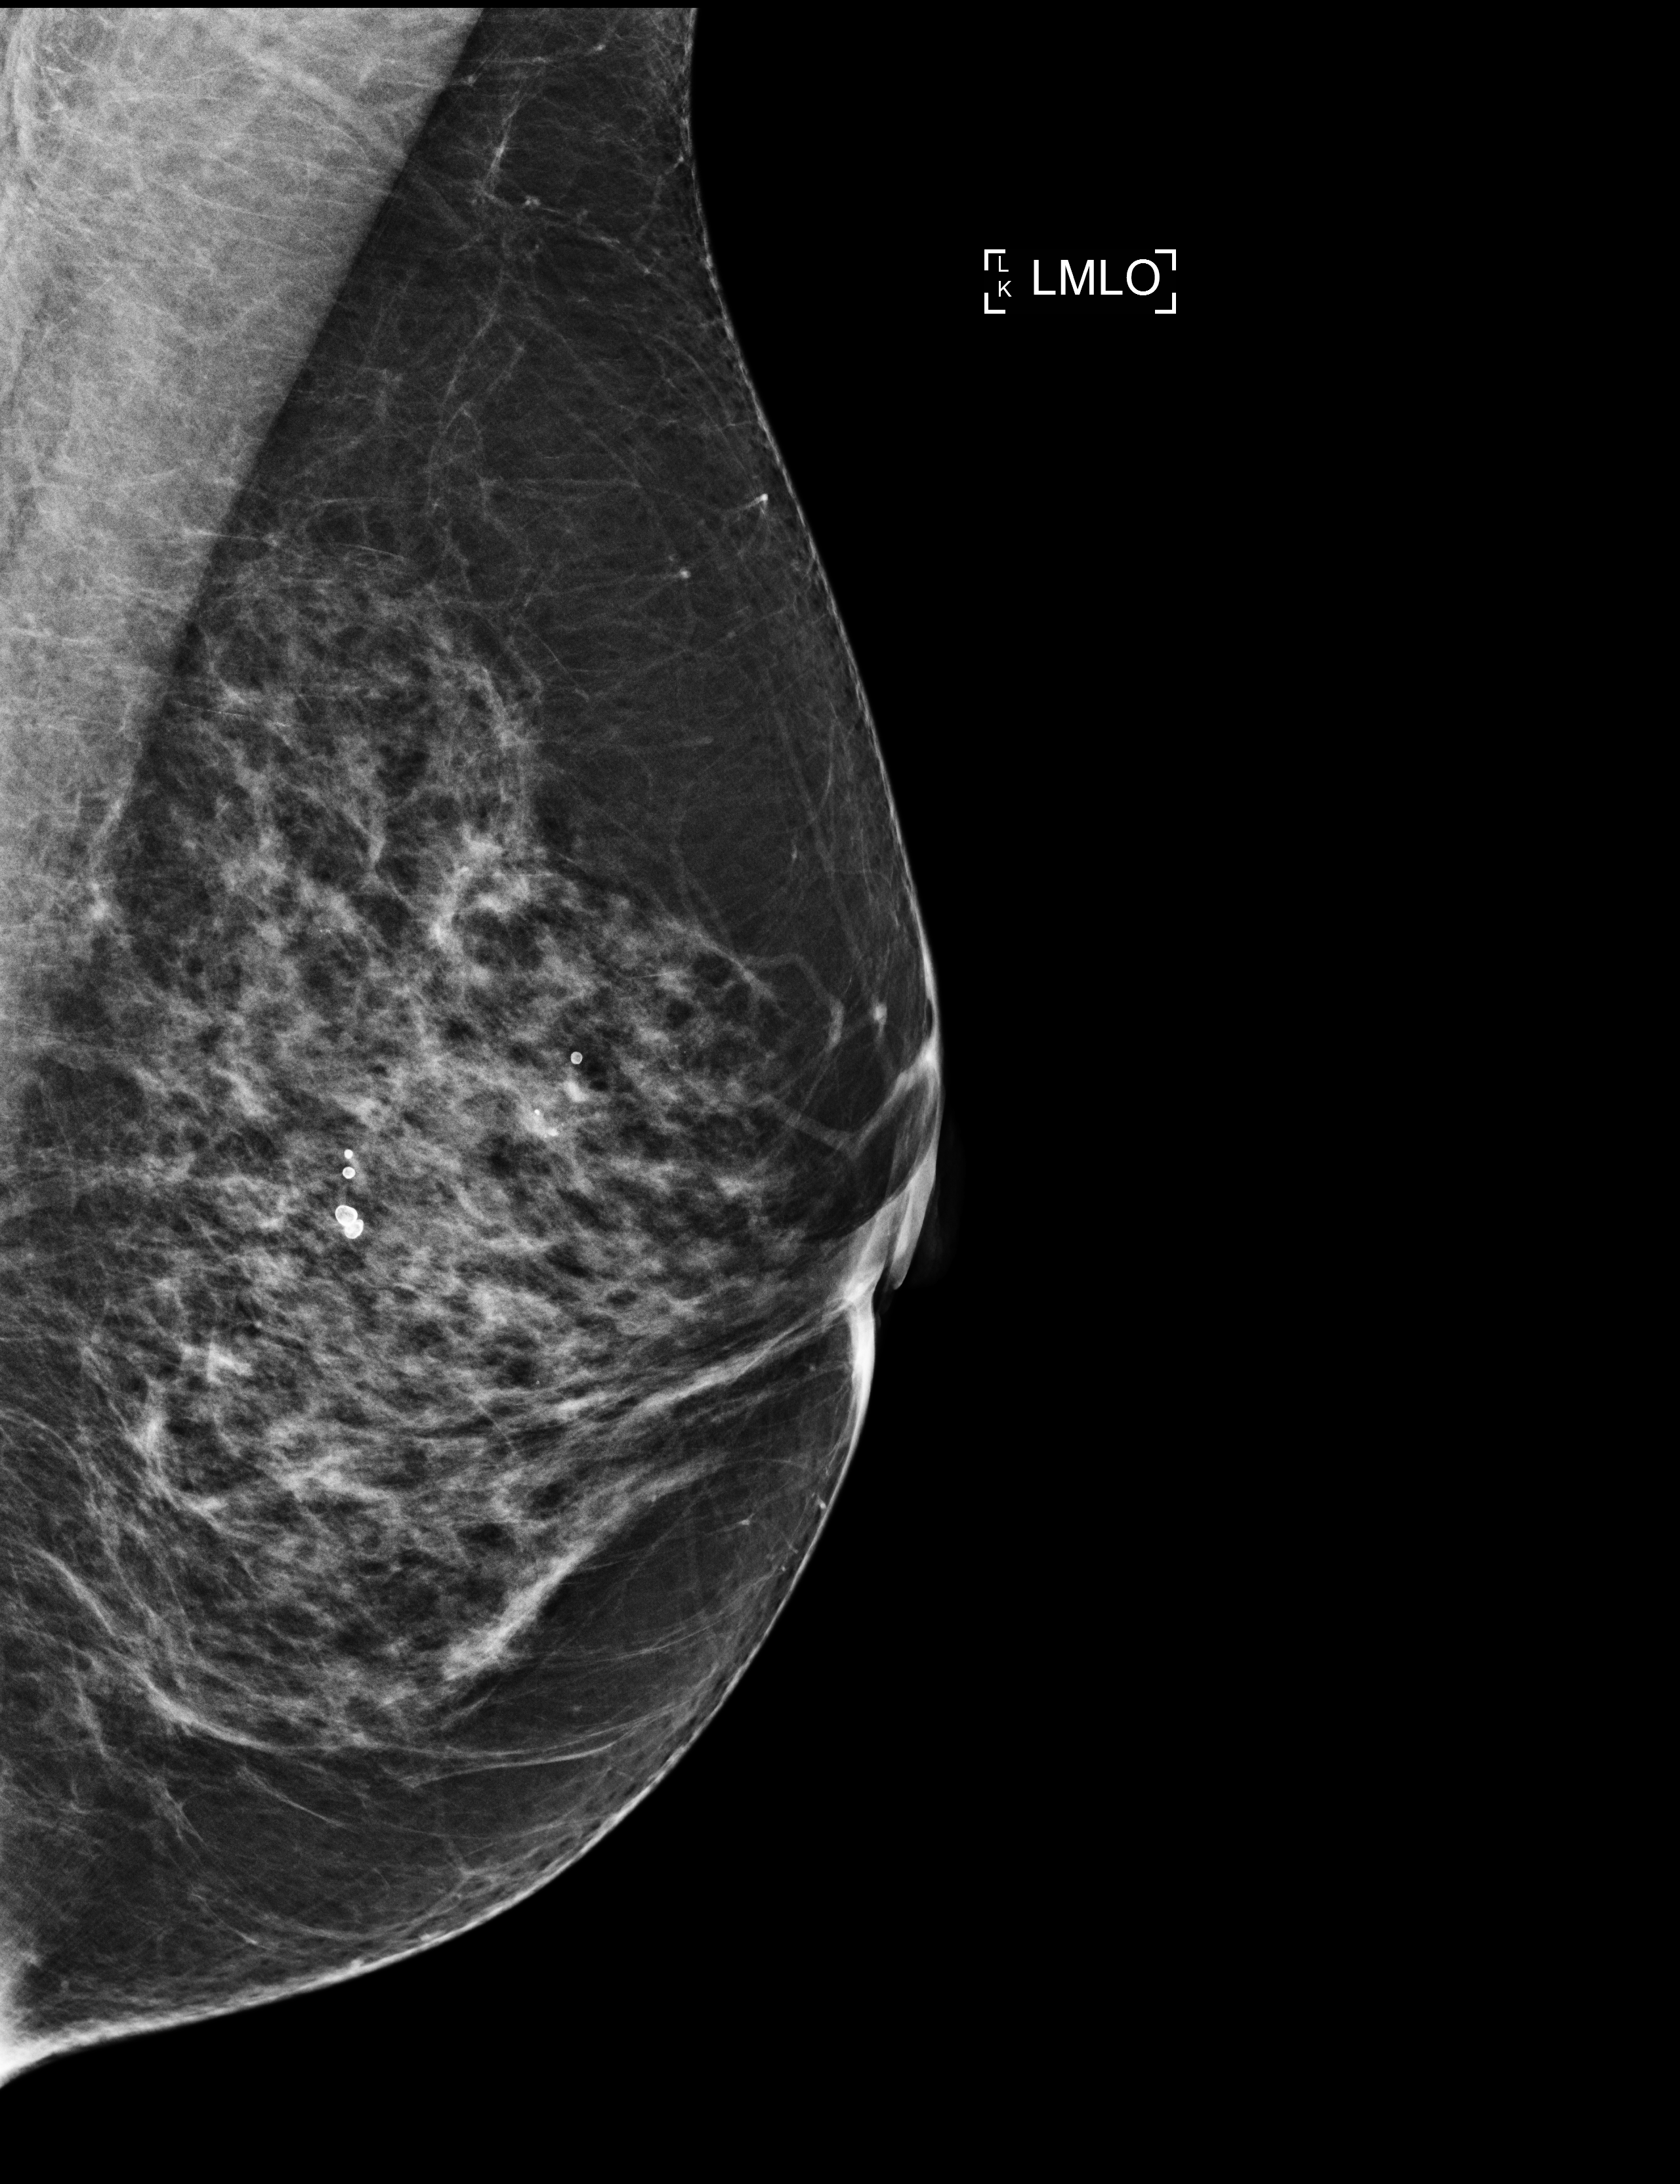
Annual screening mammography examination, compressed breast thickness 60 mm, system: Selenia Dimensions. Patient: female, 61 years.
Image type: full-field digital mammogram. Breast: left. Projection: mediolateral oblique (MLO) view.